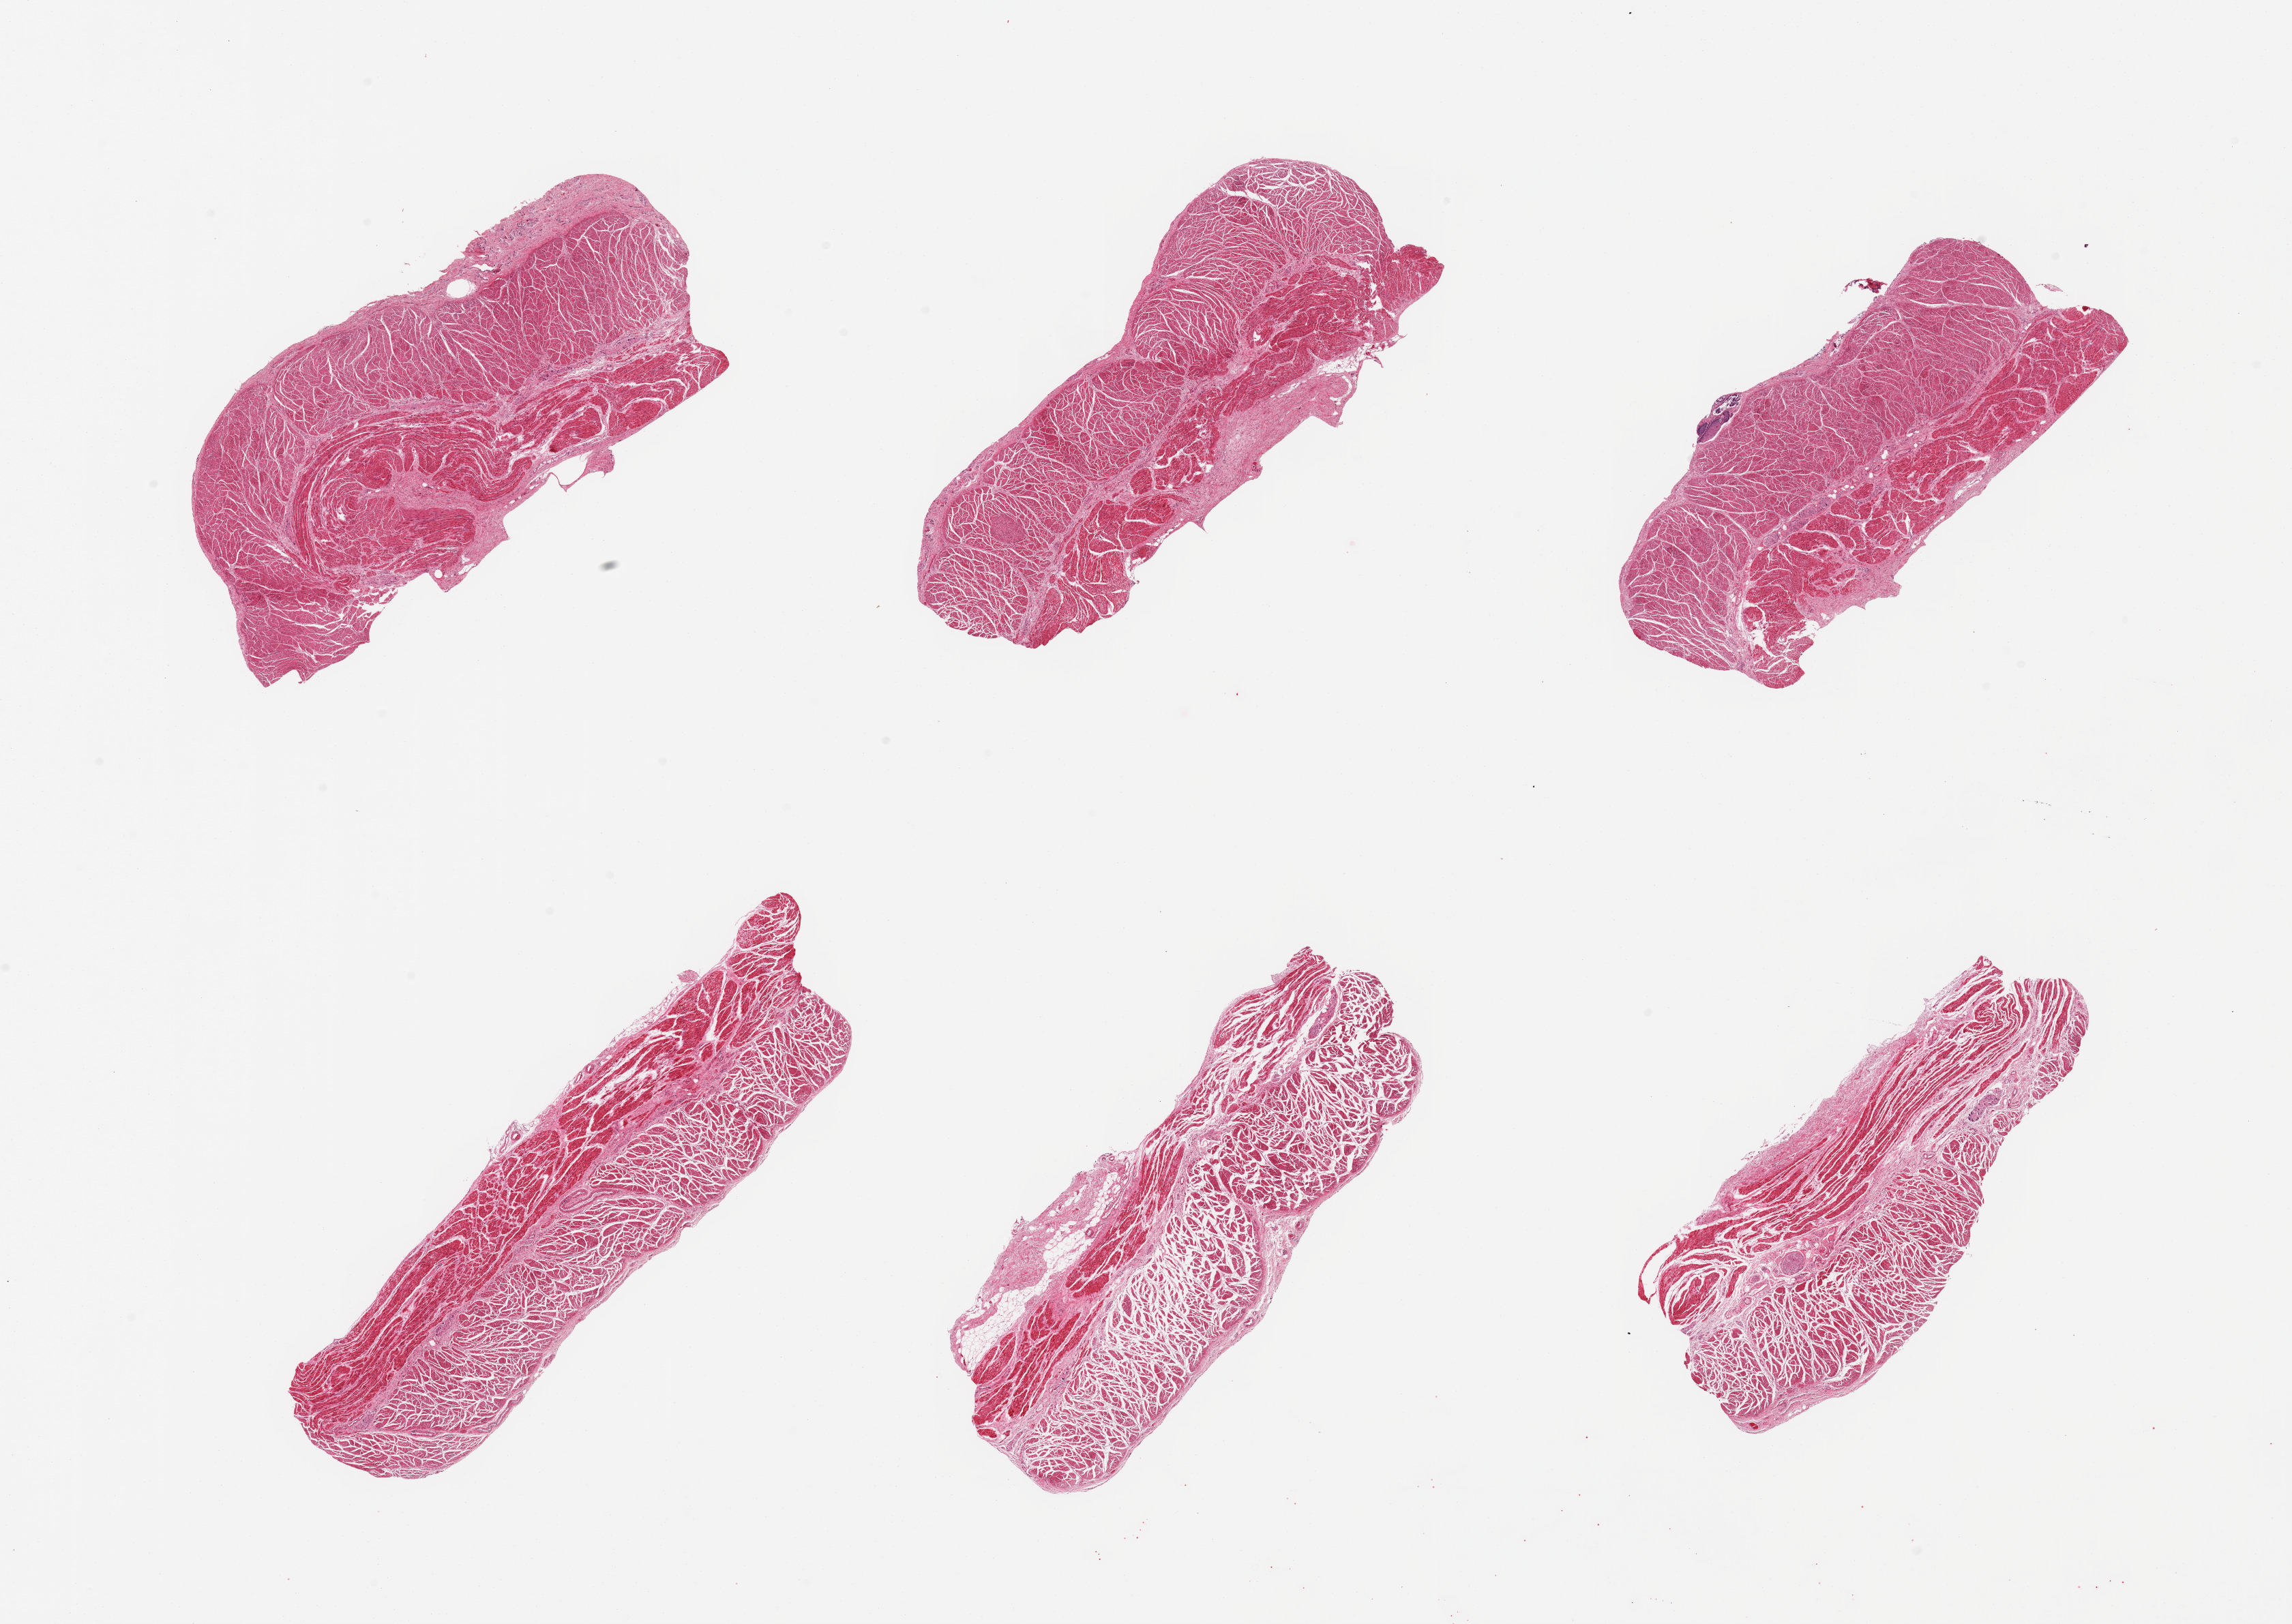
Digitized H&E-stained section, brightfield — a low-resolution overview of the entire scanned area, about 26.6 x 18.8 mm, PAXgene-fixed paraffin-embedded (PFPE) section, sampled site (target tissue): esophageal muscle, donor tissue sample.
Pathologist's review note for this sample: 6 pieces; well dissected muscle.